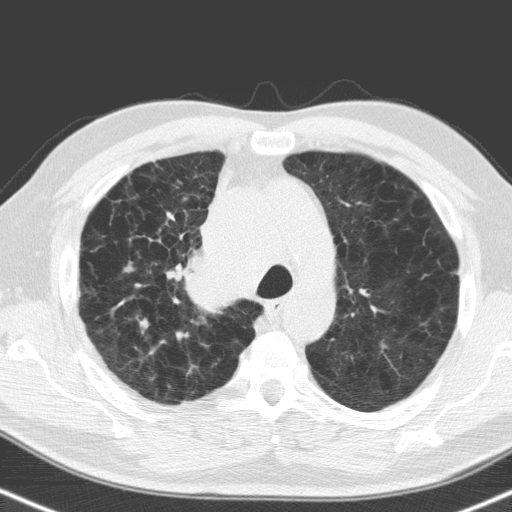
Low-dose screening chest CT, one axial slice; slice 123 of 160 in the series (ordered by position); lung window (W 1500 / L -600 HU); 512 × 512 image matrix.
Outlined on this slice (outlined manually by an expert reader):
- lesion 1 (tumor, hilum of right lung): bounding box [x1, y1, x2, y2] px = [186, 249, 245, 308]